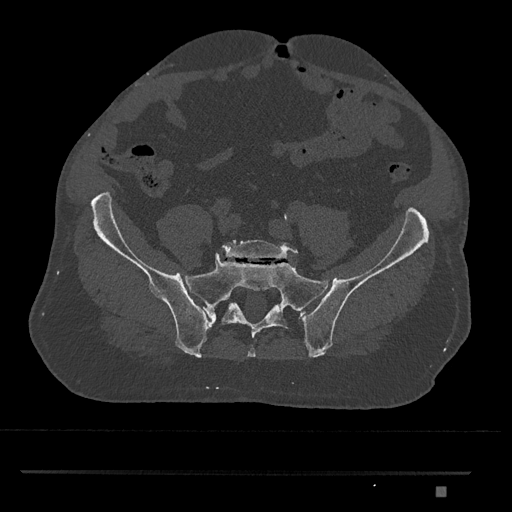
CT including the spine, one axial slice; slice 506 of 1134 in the series (ordered by position); reconstruction kernel Br40s/3; 120 kVp; bone window (W 1800 / L 400 HU); 0.5 mm slice thickness; 512 × 512 image matrix, field of view 429 × 429 mm. Patient: male, 65 years. Case-level facts recorded for this patient, not image findings: primary cancer: prostate.
Structures marked on this image (semi-automatically segmented with operator editing):
- L5 vertebra: bounding box [x1, y1, x2, y2] px = [221, 239, 298, 259]